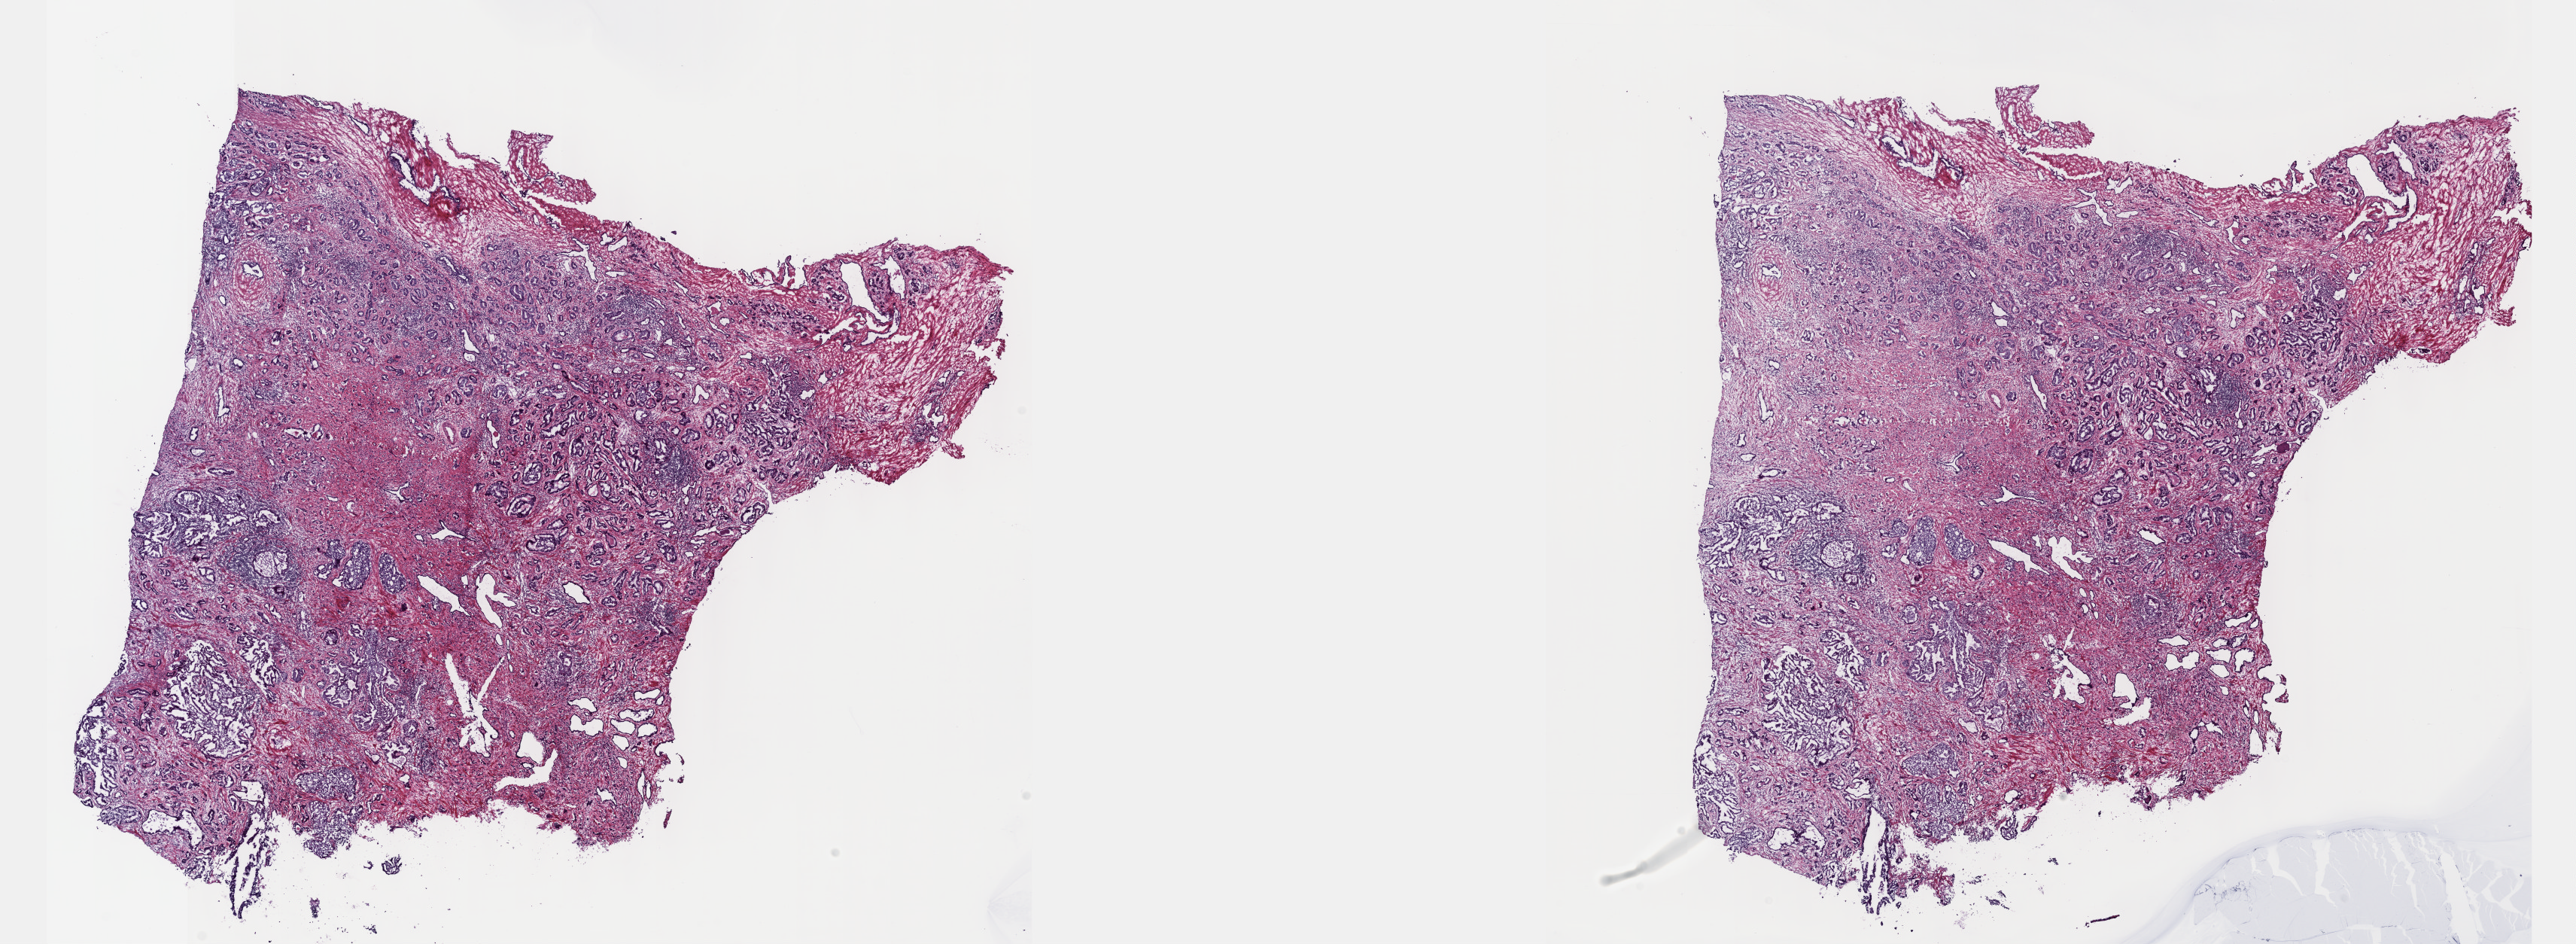
H&E whole-slide image — a low-resolution overview of the entire scanned area, about 27.7 x 10.1 mm, frozen section, sample: primary tumour, prostate. Patient: male, age at initial diagnosis 56 years. Gleason score: 8 (3+5). Pathologist review of this section (percent, as recorded): tumour cells 50%, tumour nuclei 82%, normal cells 1%, stromal cells 47%, necrosis 2%. Infiltration values recorded for this section: lymphocyte infiltration 12%, monocyte infiltration 1%, neutrophil infiltration 1%.
Diagnosis: Adenocarcinoma, NOS (prostate gland). Lymph nodes positive (case pathology): 0 of 12 examined.